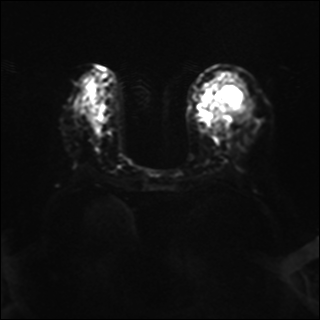
Breast MRI, one axial slice; slice 17 of 37 in the series (ordered by position); diffusion-weighted series; image 2 of 4 stored at this slice position (different b-values; order by instance number); 1.5 T; 4 mm slice thickness; 320 × 320 image matrix, field of view 320 × 320 mm. Female patient.
Annotated regions visible in this slice (manually delineated by an expert):
- tumour on diffusion-weighted imaging: bounding box [x1, y1, x2, y2] px = [216, 83, 247, 120]